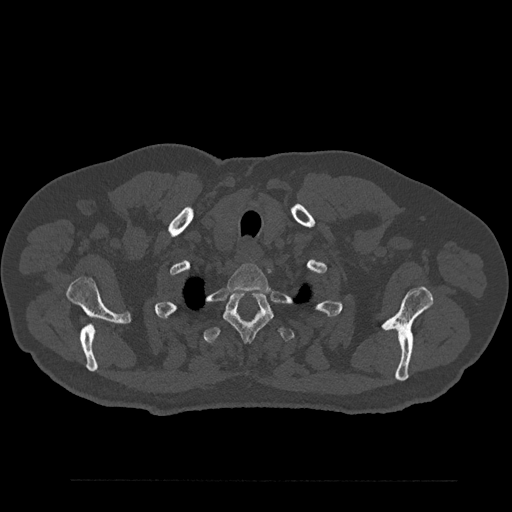
CT including the spine, one axial slice; slice 719 of 797 in the series (ordered by position); 120 kVp; bone window (W 1800 / L 400 HU); 0.5 mm slice thickness; 512 × 512 image matrix. Male patient, age 61 years. From the clinical record (not read from this slice): primary cancer: prostate.
Outlined on this slice (semi-automatically segmented with operator editing):
- T1 vertebra: bounding box (x1, y1, x2, y2) in pixels: (227, 264, 269, 292)
- T2 vertebra: (223, 292, 273, 342)
- T3 vertebra: (203, 326, 294, 344)